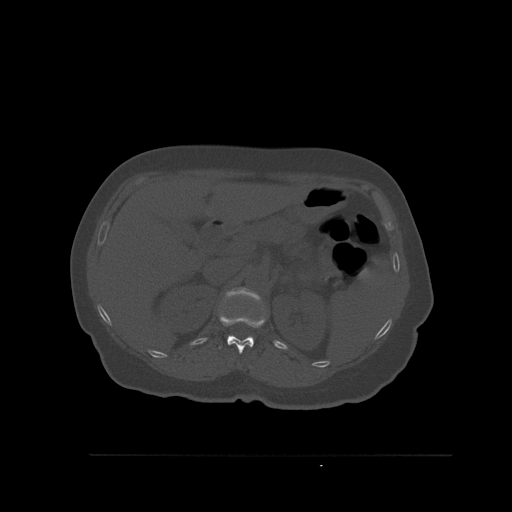
CT including the spine, one axial slice. Position 281 of 527 along the scan axis. Bone window (W 1800 / L 400 HU). 1.5 mm slice thickness. 512 × 512 image matrix, field of view 470 × 470 mm. Female patient, age 73 years. From the clinical record (not read from this slice): primary cancer: breast; vertebrae with lytic lesions (as recorded): L2.
Annotated regions visible in this slice (semi-automatic segmentation, software-assisted and operator-edited):
- L1 vertebra: bounding box [x1, y1, x2, y2] px = [225, 287, 261, 302]
- T12 vertebra: [219, 315, 265, 354]